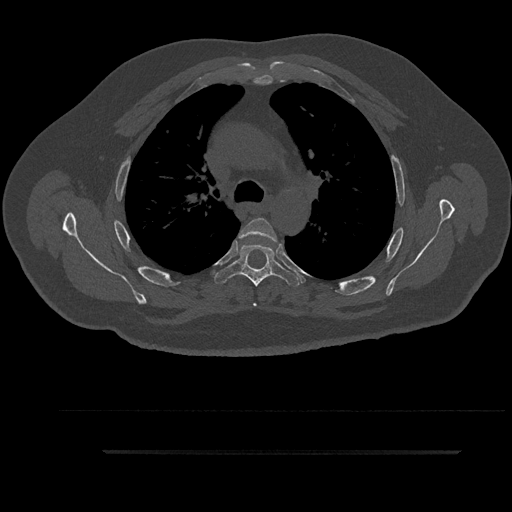
CT including the spine, one axial slice. Slice 641 of 797 in the series (ordered by position). Reconstruction kernel Br40s/3. 120 kVp. Bone window (W 1800 / L 400 HU). 0.5 mm slice thickness. 512 × 512 image matrix, field of view 432 × 432 mm. Patient: male, 63 years. From the clinical record (not read from this slice): primary cancer: renal; vertebrae with lytic lesions (as recorded): T8.
Structures marked on this image (semi-automatic segmentation, software-assisted and operator-edited):
- T3 vertebra: bounding box <245,257,247,259> (left, top, right, bottom; pixels)
- T4 vertebra: <238,218,280,306>
- T5 vertebra: <215,244,300,289>